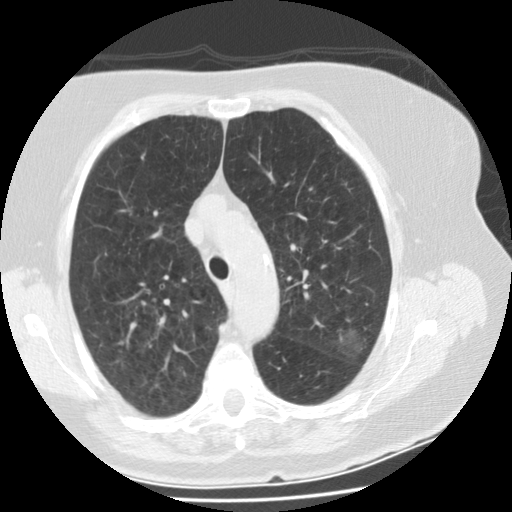
Low-dose screening chest CT, one axial slice; slice 114 of 151 in the series (ordered by position); reconstruction kernel STANDARD; 120 kVp; one of 2 acquisitions stored at this slice position; lung window (W 1500 / L -600 HU); 2.5 mm slice thickness; 512 × 512 image matrix, field of view 321 × 321 mm.
Outlined on this slice (outlined manually by an expert reader):
- lesion 1 (tumor, upper lobe of left lung): bounding box [x1, y1, x2, y2] px = [334, 329, 366, 357]